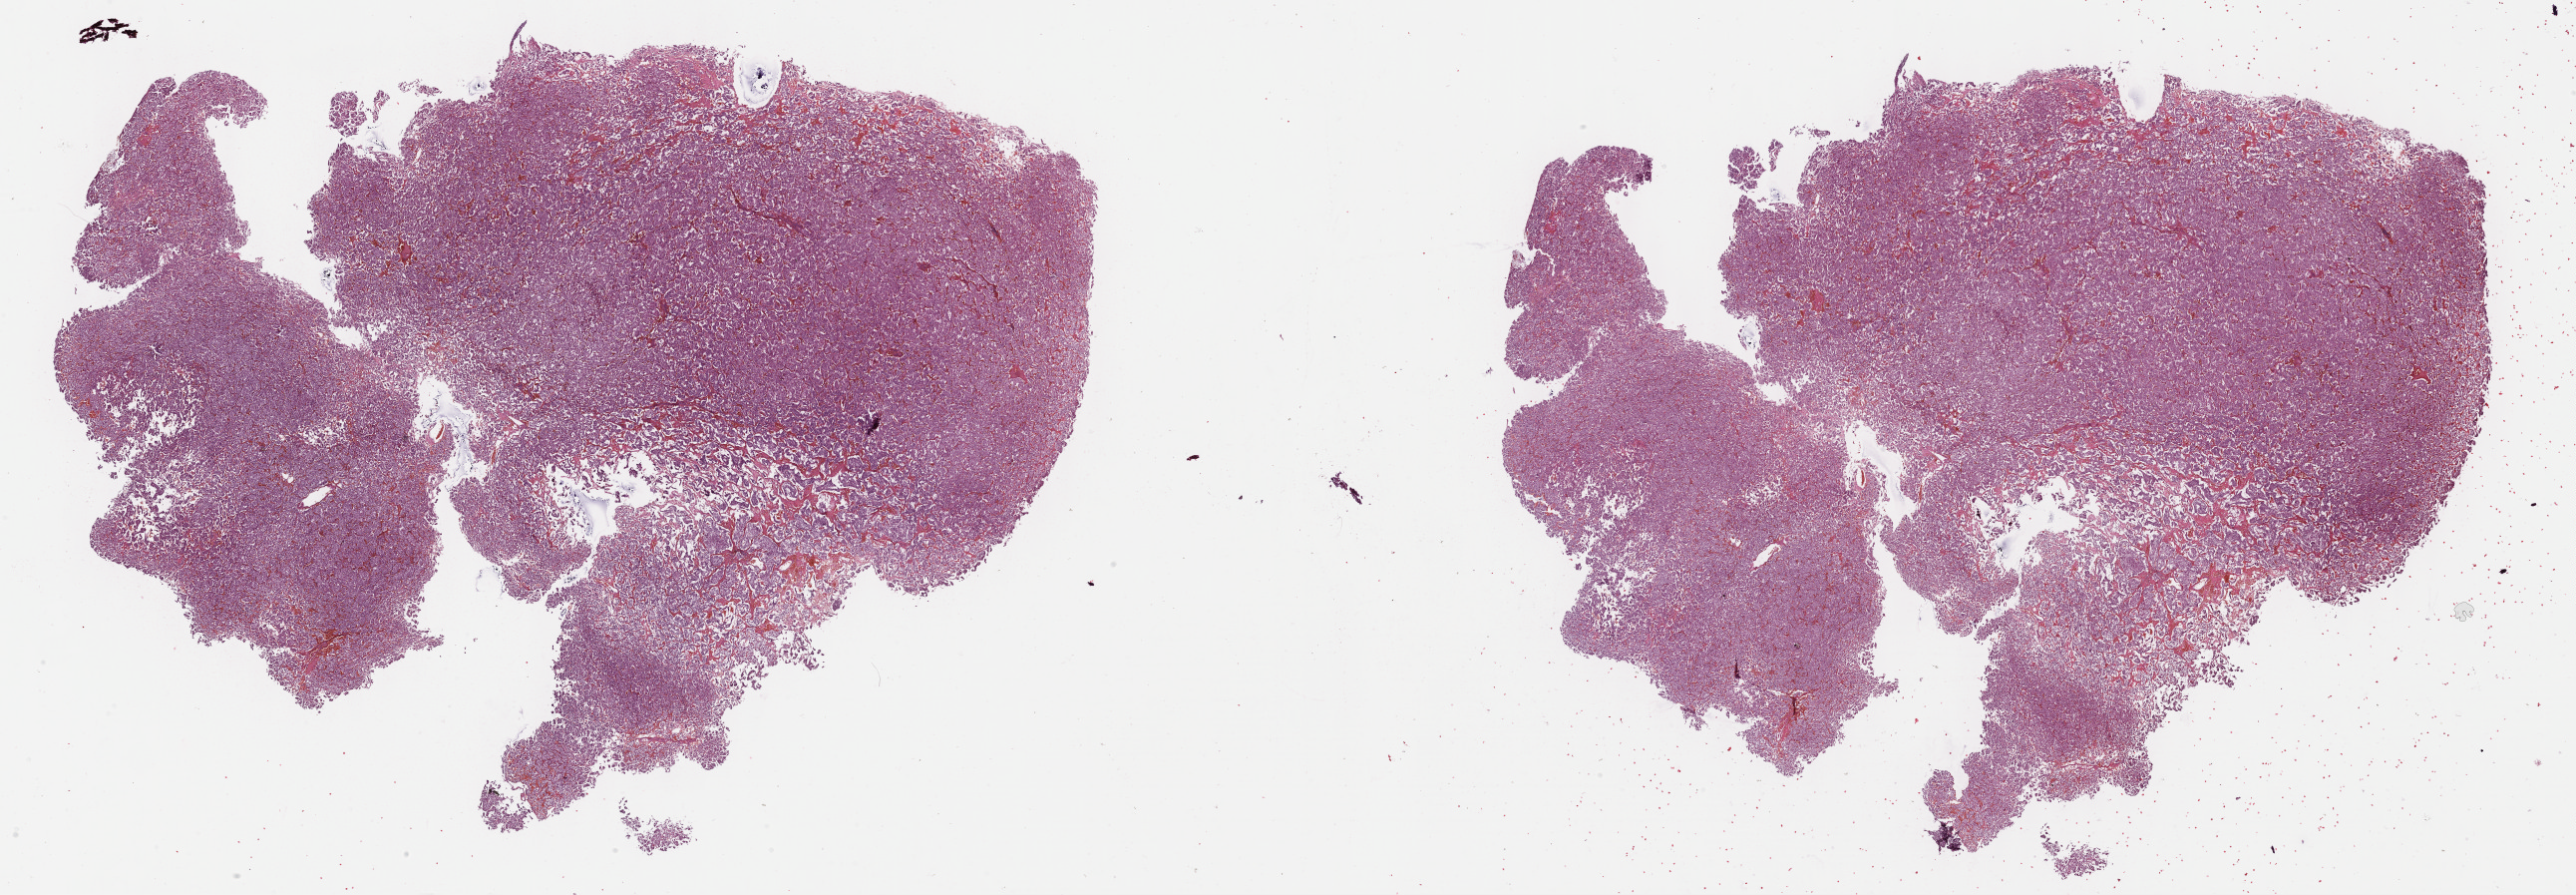
H&E-stained whole-slide image — shown as a low-resolution overview of the whole scanned area (about 41.8 x 14.5 mm, acquisition: 40x scan), formalin-fixed paraffin-embedded (FFPE) diagnostic section, sample: primary tumour, adrenal gland. Female patient; age at initial diagnosis 32 years.
Diagnosis: Pheochromocytoma, NOS. Laterality: right.